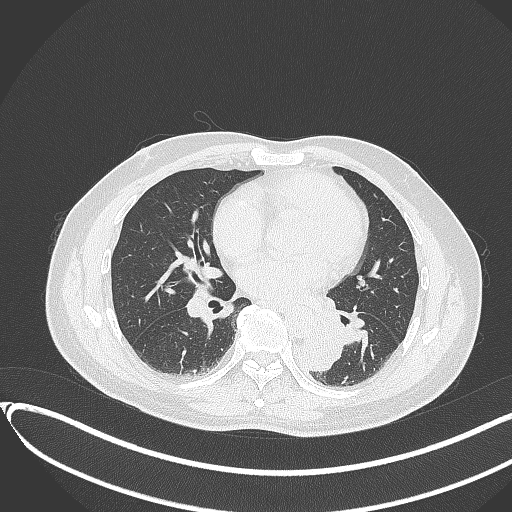
Chest CT, one axial slice. Slice 154 of 417 in the series (ordered by position). Reconstruction kernel B70f. 120 kVp. Lung window (W 1500 / L -600 HU). 1 mm slice thickness. 512 × 512 image matrix, field of view 400 × 400 mm. Male patient, age 54 years. Case-level facts recorded for this patient, not image findings: clinical TNM (as recorded): T3 N0 M0.
Annotated regions visible in this slice (bounding box drawn by a radiologist):
- lung tumour (recorded histology: squamous cell carcinoma): bounding box <301,325,347,373> (left, top, right, bottom; pixels)